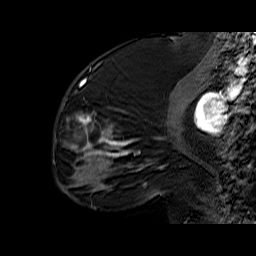
Breast MRI (dynamic contrast-enhanced), one sagittal slice; position 23 of 60 along the scan axis; dynamic contrast-enhanced series, time point 2 of 6 at this slice position (early post-contrast); 1.5 T; TE 6.4 ms, TR 32.9 ms; 4 mm slice thickness; 256 × 256 image matrix. Female patient. Case-level facts recorded for this patient, not image findings: setting: breast cancer imaged before/during neoadjuvant chemotherapy; receptor status: triple-negative.
Outlined on this slice (semi-automatically segmented with operator editing):
- analysis volume of interest (the breast-tissue region the enhancement analysis was run in; not a lesion): bounding box <56,65,159,174> (left, top, right, bottom; pixels)
- tumour enhancement mask (voxels above the 100 % enhancement threshold inside the analysis volume of interest): <67,80,159,171>